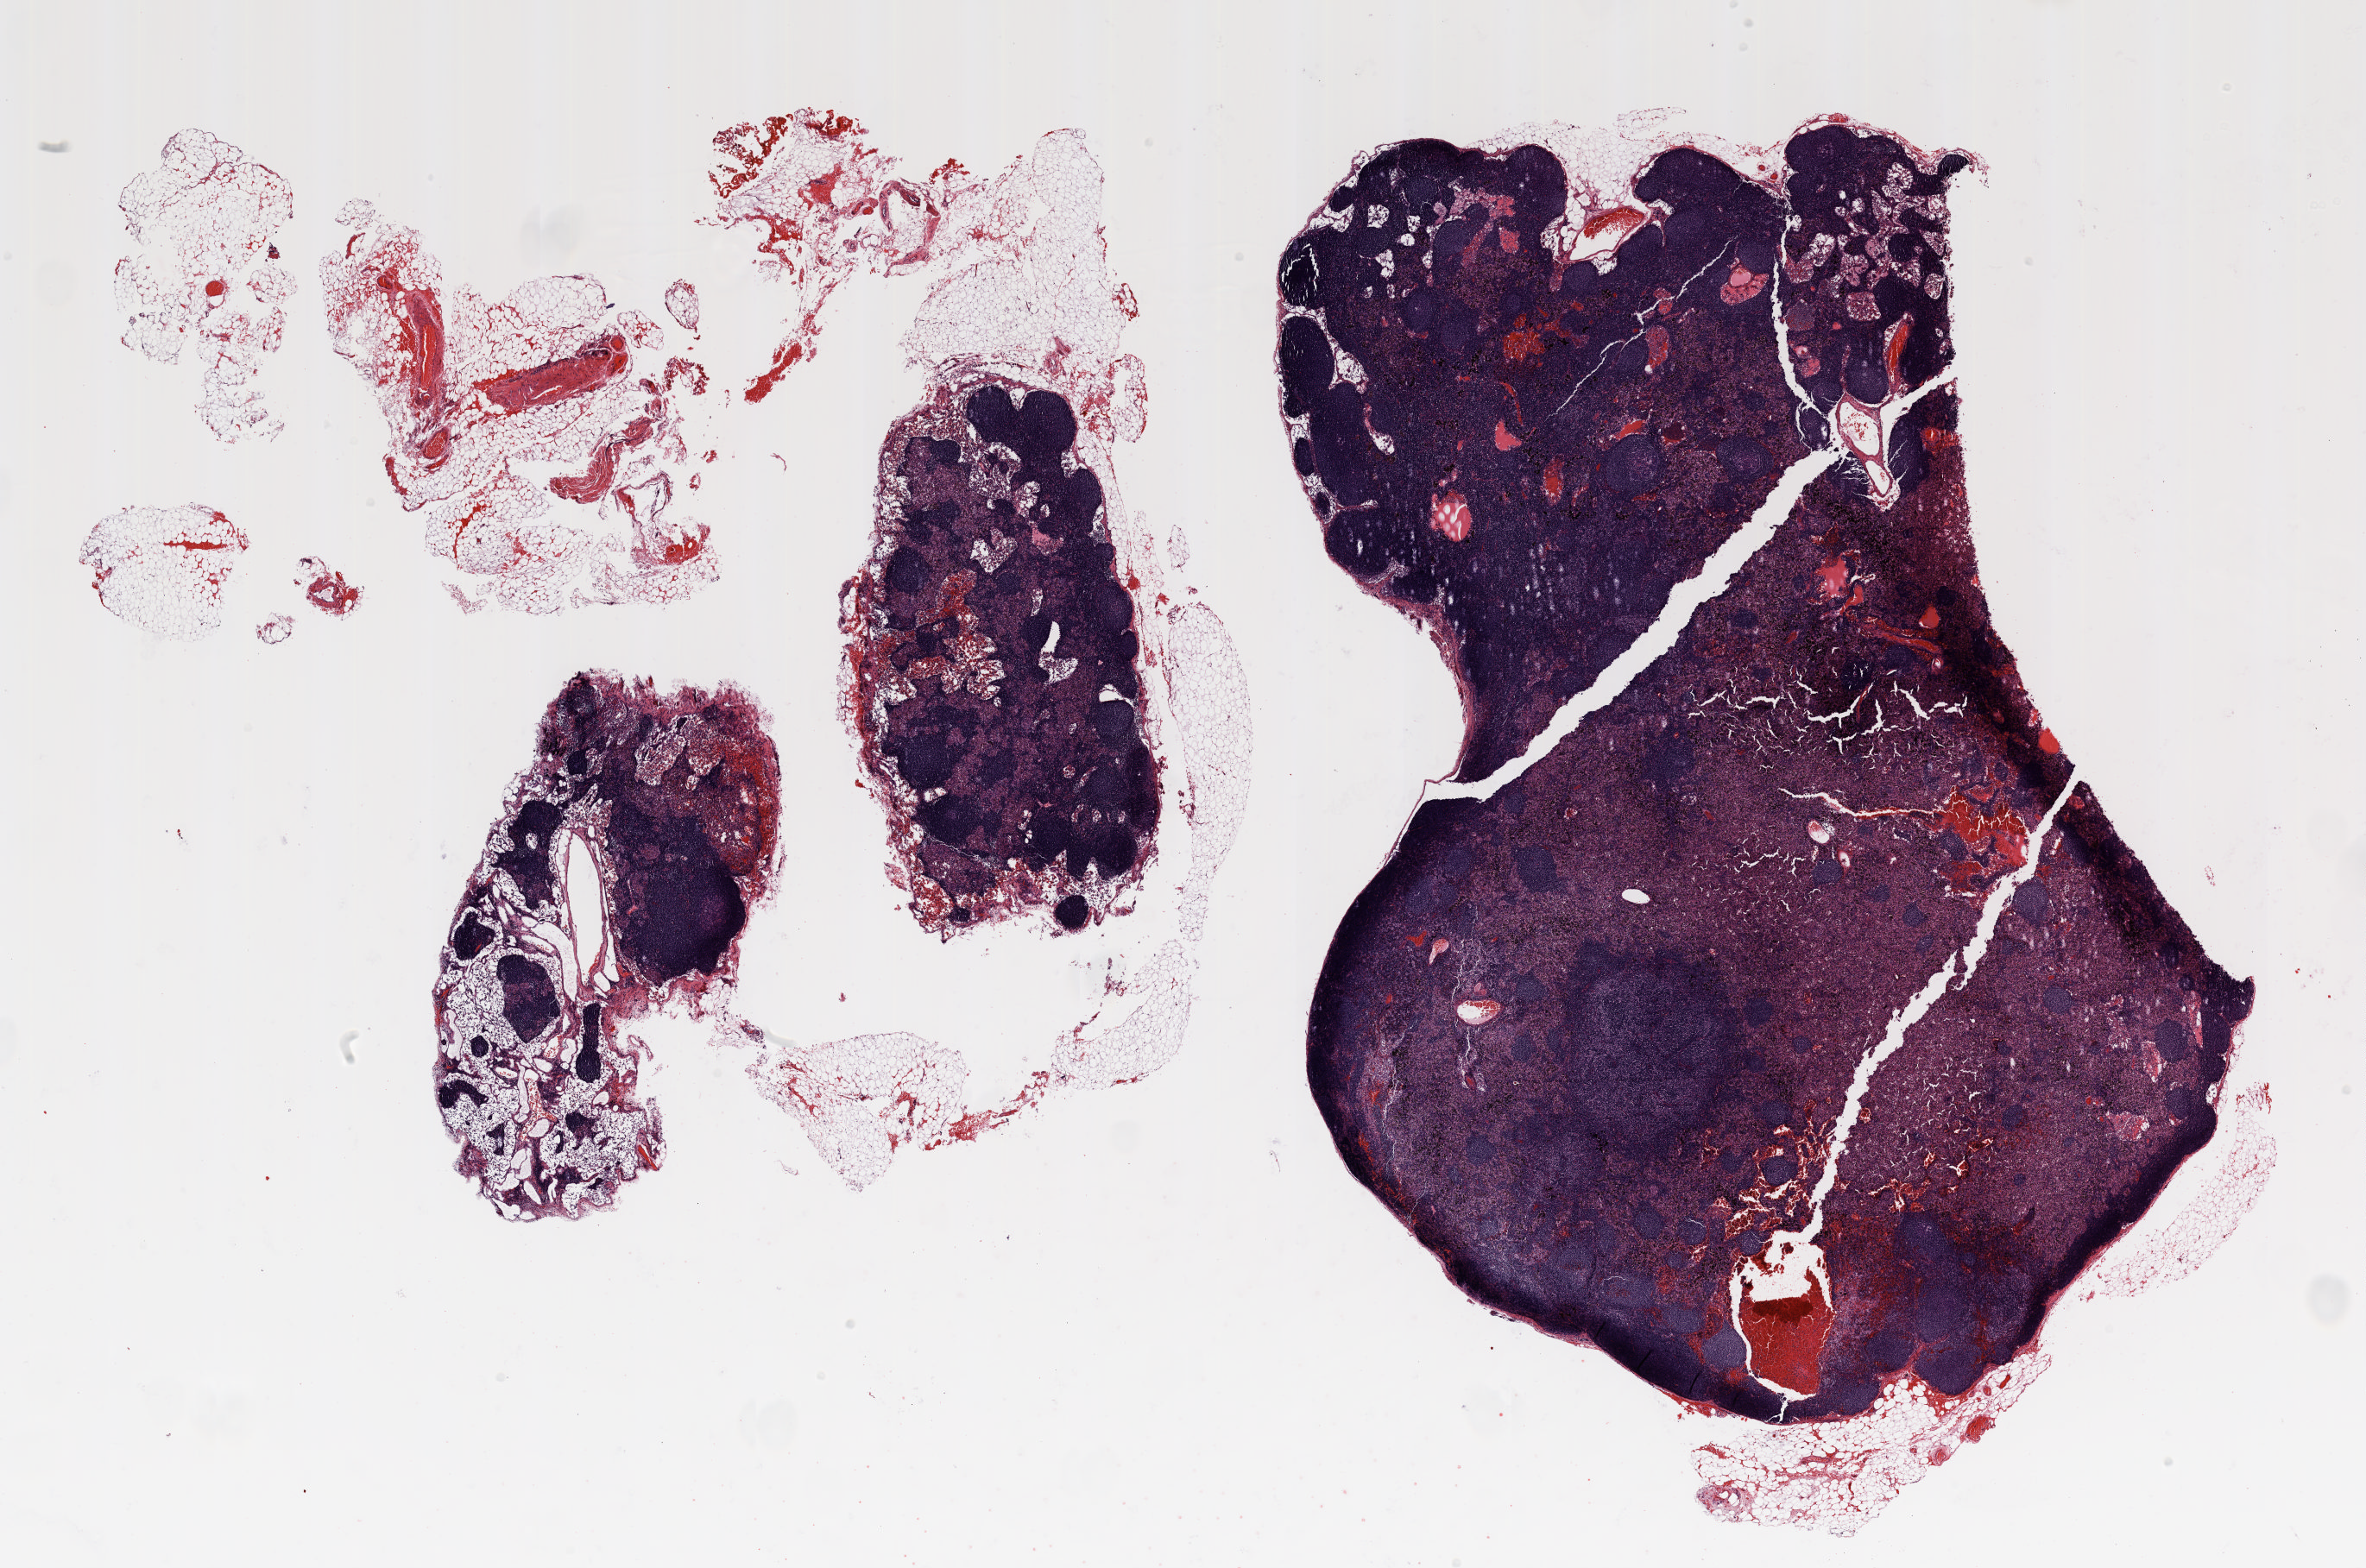
H&E whole-slide image — shown as a low-resolution overview of the whole scanned area (about 22.0 x 14.6 mm, acquisition: 20x scan), formalin-fixed paraffin-embedded (FFPE) section, lung. Female patient, aged 60 at enrolment. Current smoker at enrolment. Grade: poorly differentiated (G3).
• tumour size (pathology): 10 mm
• stage (AJCC 6th edition): IA
• primary tumour location (clinical record): left upper lobe
• participant's lung-cancer diagnosis: Non-small cell carcinoma (ICD-O-3 8046/3)